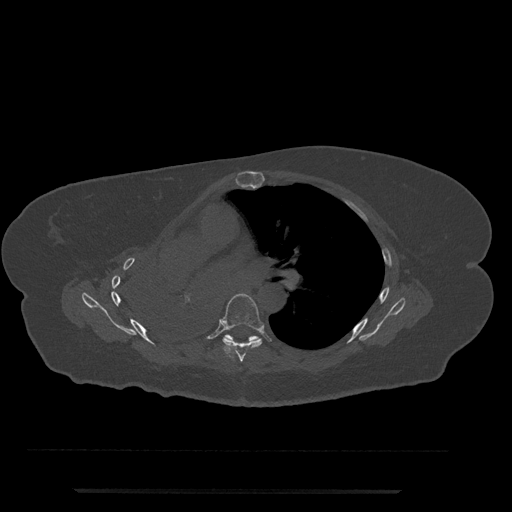
CT including the spine, one axial slice. Position 483 of 797 along the scan axis. Reconstruction kernel Br40s/3. 120 kVp. Bone window (W 1800 / L 400 HU). 0.5 mm slice thickness. 512 × 512 image matrix. Female patient, age 51 years. From the clinical record (not read from this slice): primary cancer: neuro.
Annotated regions visible in this slice (semi-automatically segmented with operator editing):
- T6 vertebra: box from (x=221, y=293) to (x=263, y=362) px
- T7 vertebra: (x=225, y=334)–(x=260, y=341)